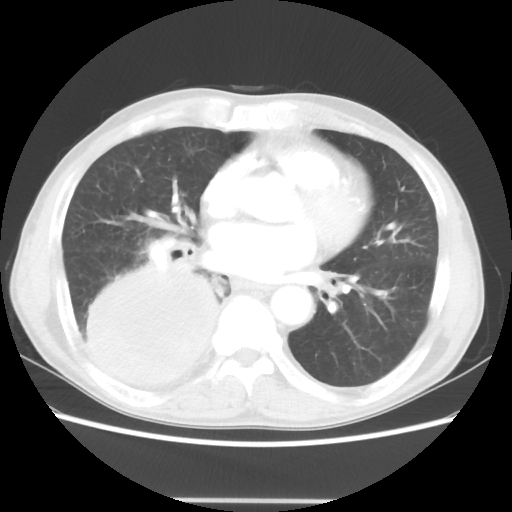
Chest CT, one axial slice; position 19 of 48 along the scan axis; reconstruction kernel STANDARD; lung window (W 1500 / L -600 HU); 5 mm slice thickness; 512 × 512 image matrix, field of view 361 × 361 mm. Male patient, age 66 years. Case-level facts recorded for this patient, not image findings: clinical TNM (as recorded): T4 N1 M1.
Outlined on this slice (bounding box drawn by a radiologist):
- lung tumour (recorded histology: small cell carcinoma): box from (x=81, y=253) to (x=222, y=411) px